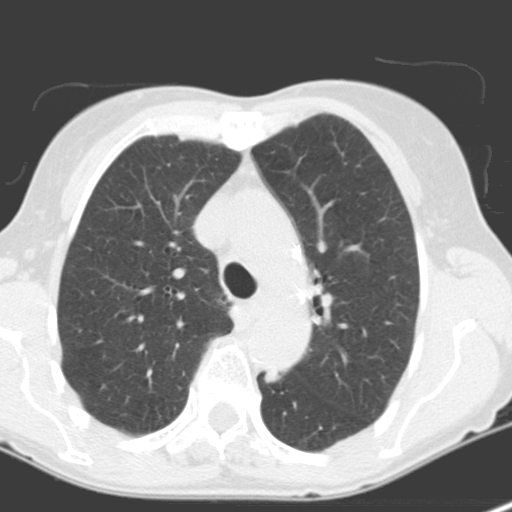
Low-dose screening chest CT, one axial slice. Slice 103 of 141 in the series (ordered by position). Lung window (W 1500 / L -600 HU). 512 × 512 image matrix, field of view 262 × 262 mm.
Structures marked on this image (outlined manually by an expert reader):
- lesion 1 (tumor, lower lobe of left lung): box from (x=265, y=369) to (x=281, y=383) px